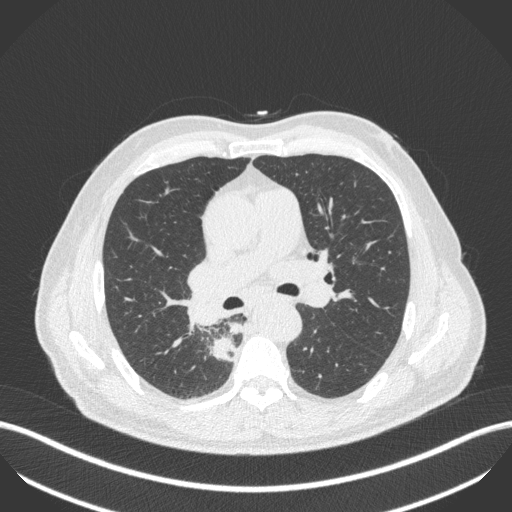
Chest CT, one axial slice. Position 276 of 451 along the scan axis. Reconstruction kernel B31f. 100 kVp. Lung window (W 1500 / L -600 HU). 1 mm slice thickness. 512 × 512 image matrix. Male patient, age 61 years. From the clinical record (not read from this slice): clinical TNM (as recorded): T1 N0 M0.
Outlined on this slice (rectangle marked by the reading radiologist):
- lung tumour (recorded histology: small cell carcinoma): bounding box (x1, y1, x2, y2) in pixels: (205, 334, 240, 366)